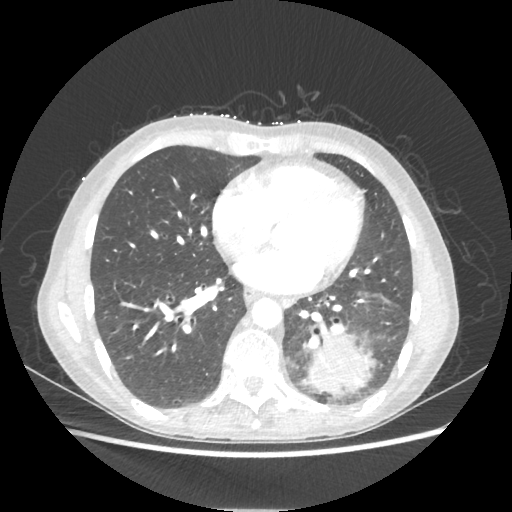
Chest CT, one axial slice; slice 87 of 221 in the series (ordered by position); 80 kVp; lung window (W 1500 / L -600 HU); 1.25 mm slice thickness; 512 × 512 image matrix, field of view 360 × 360 mm. Female patient, age 53 years. From the clinical record (not read from this slice): clinical TNM (as recorded): T3 N0 M0.
Annotated regions visible in this slice (rectangle marked by the reading radiologist):
- lung tumour (recorded histology: adenocarcinoma): bounding box [x1, y1, x2, y2] px = [301, 330, 375, 395]